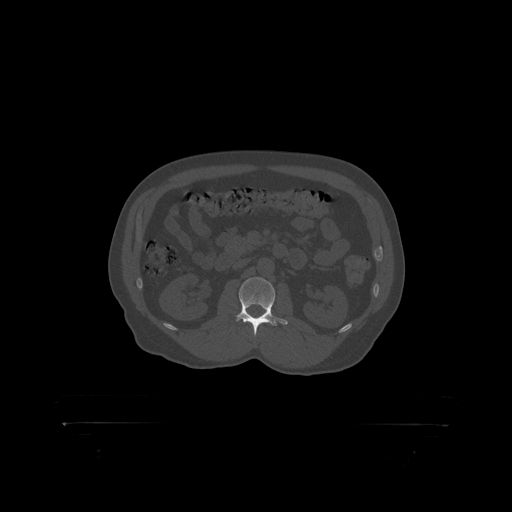
CT including the spine, one axial slice. Position 296 of 399 along the scan axis. 120 kVp. Bone window (W 1800 / L 400 HU). 1.25 mm slice thickness. 512 × 512 image matrix, field of view 650 × 650 mm. Male patient, age 46 years. Case-level facts recorded for this patient, not image findings: primary cancer: skin.
Structures marked on this image (semi-automatically segmented with operator editing):
- L2 vertebra: bounding box (x1, y1, x2, y2) in pixels: (238, 277, 276, 319)